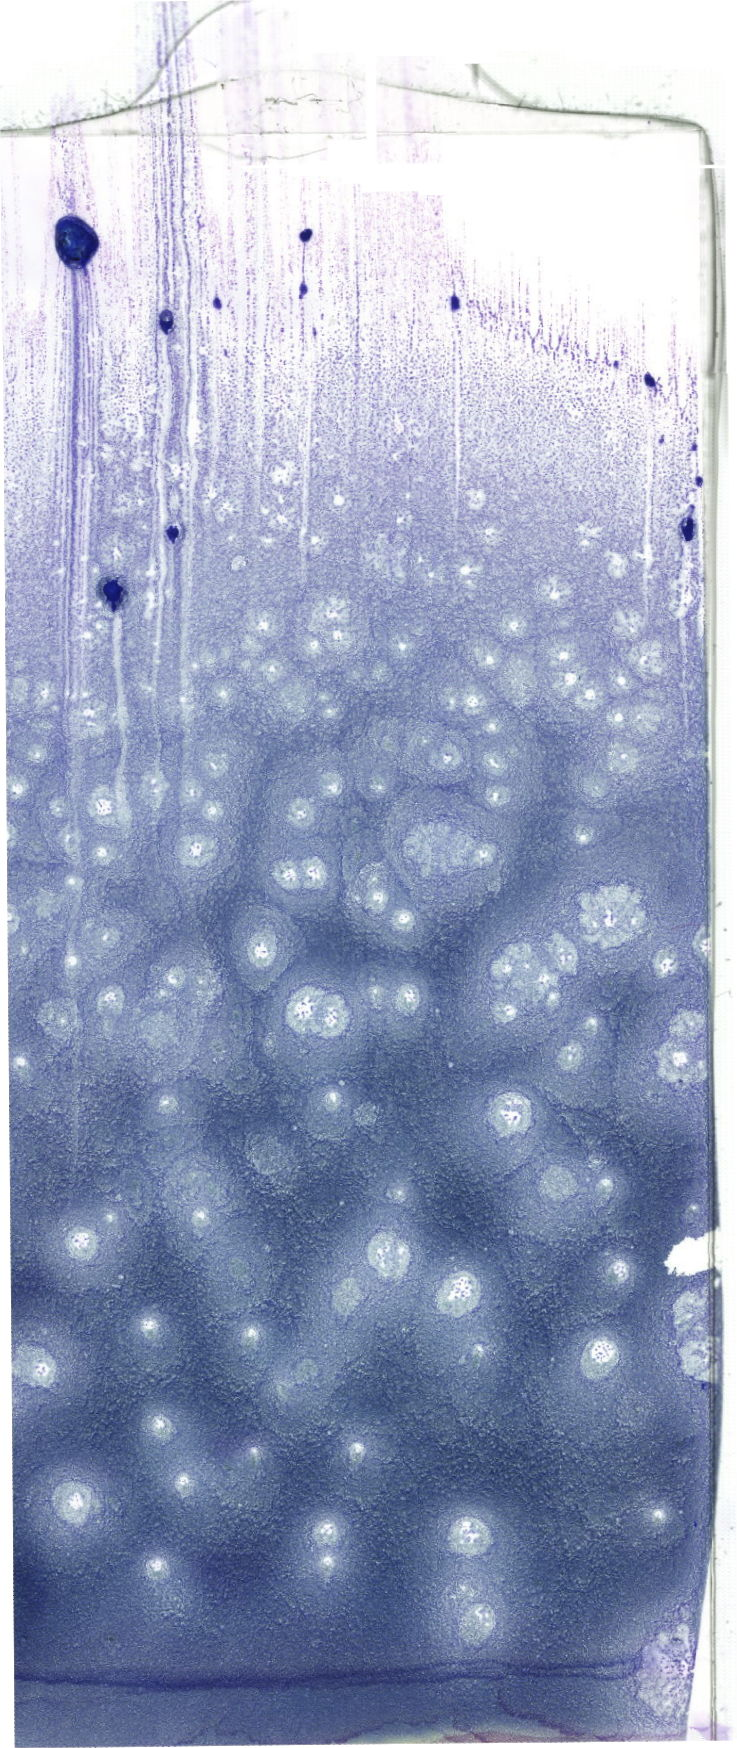
May-Grünwald-Giemsa (MGG)-stained marrow aspirate smear (whole slide), a low-resolution overview of the entire scanned area, about 20.9 x 49.5 mm. Female patient.
* diagnosis: Acute Promyelocytic Leukemia with t(15;17)(q24.1;q21.2);PML-RARA